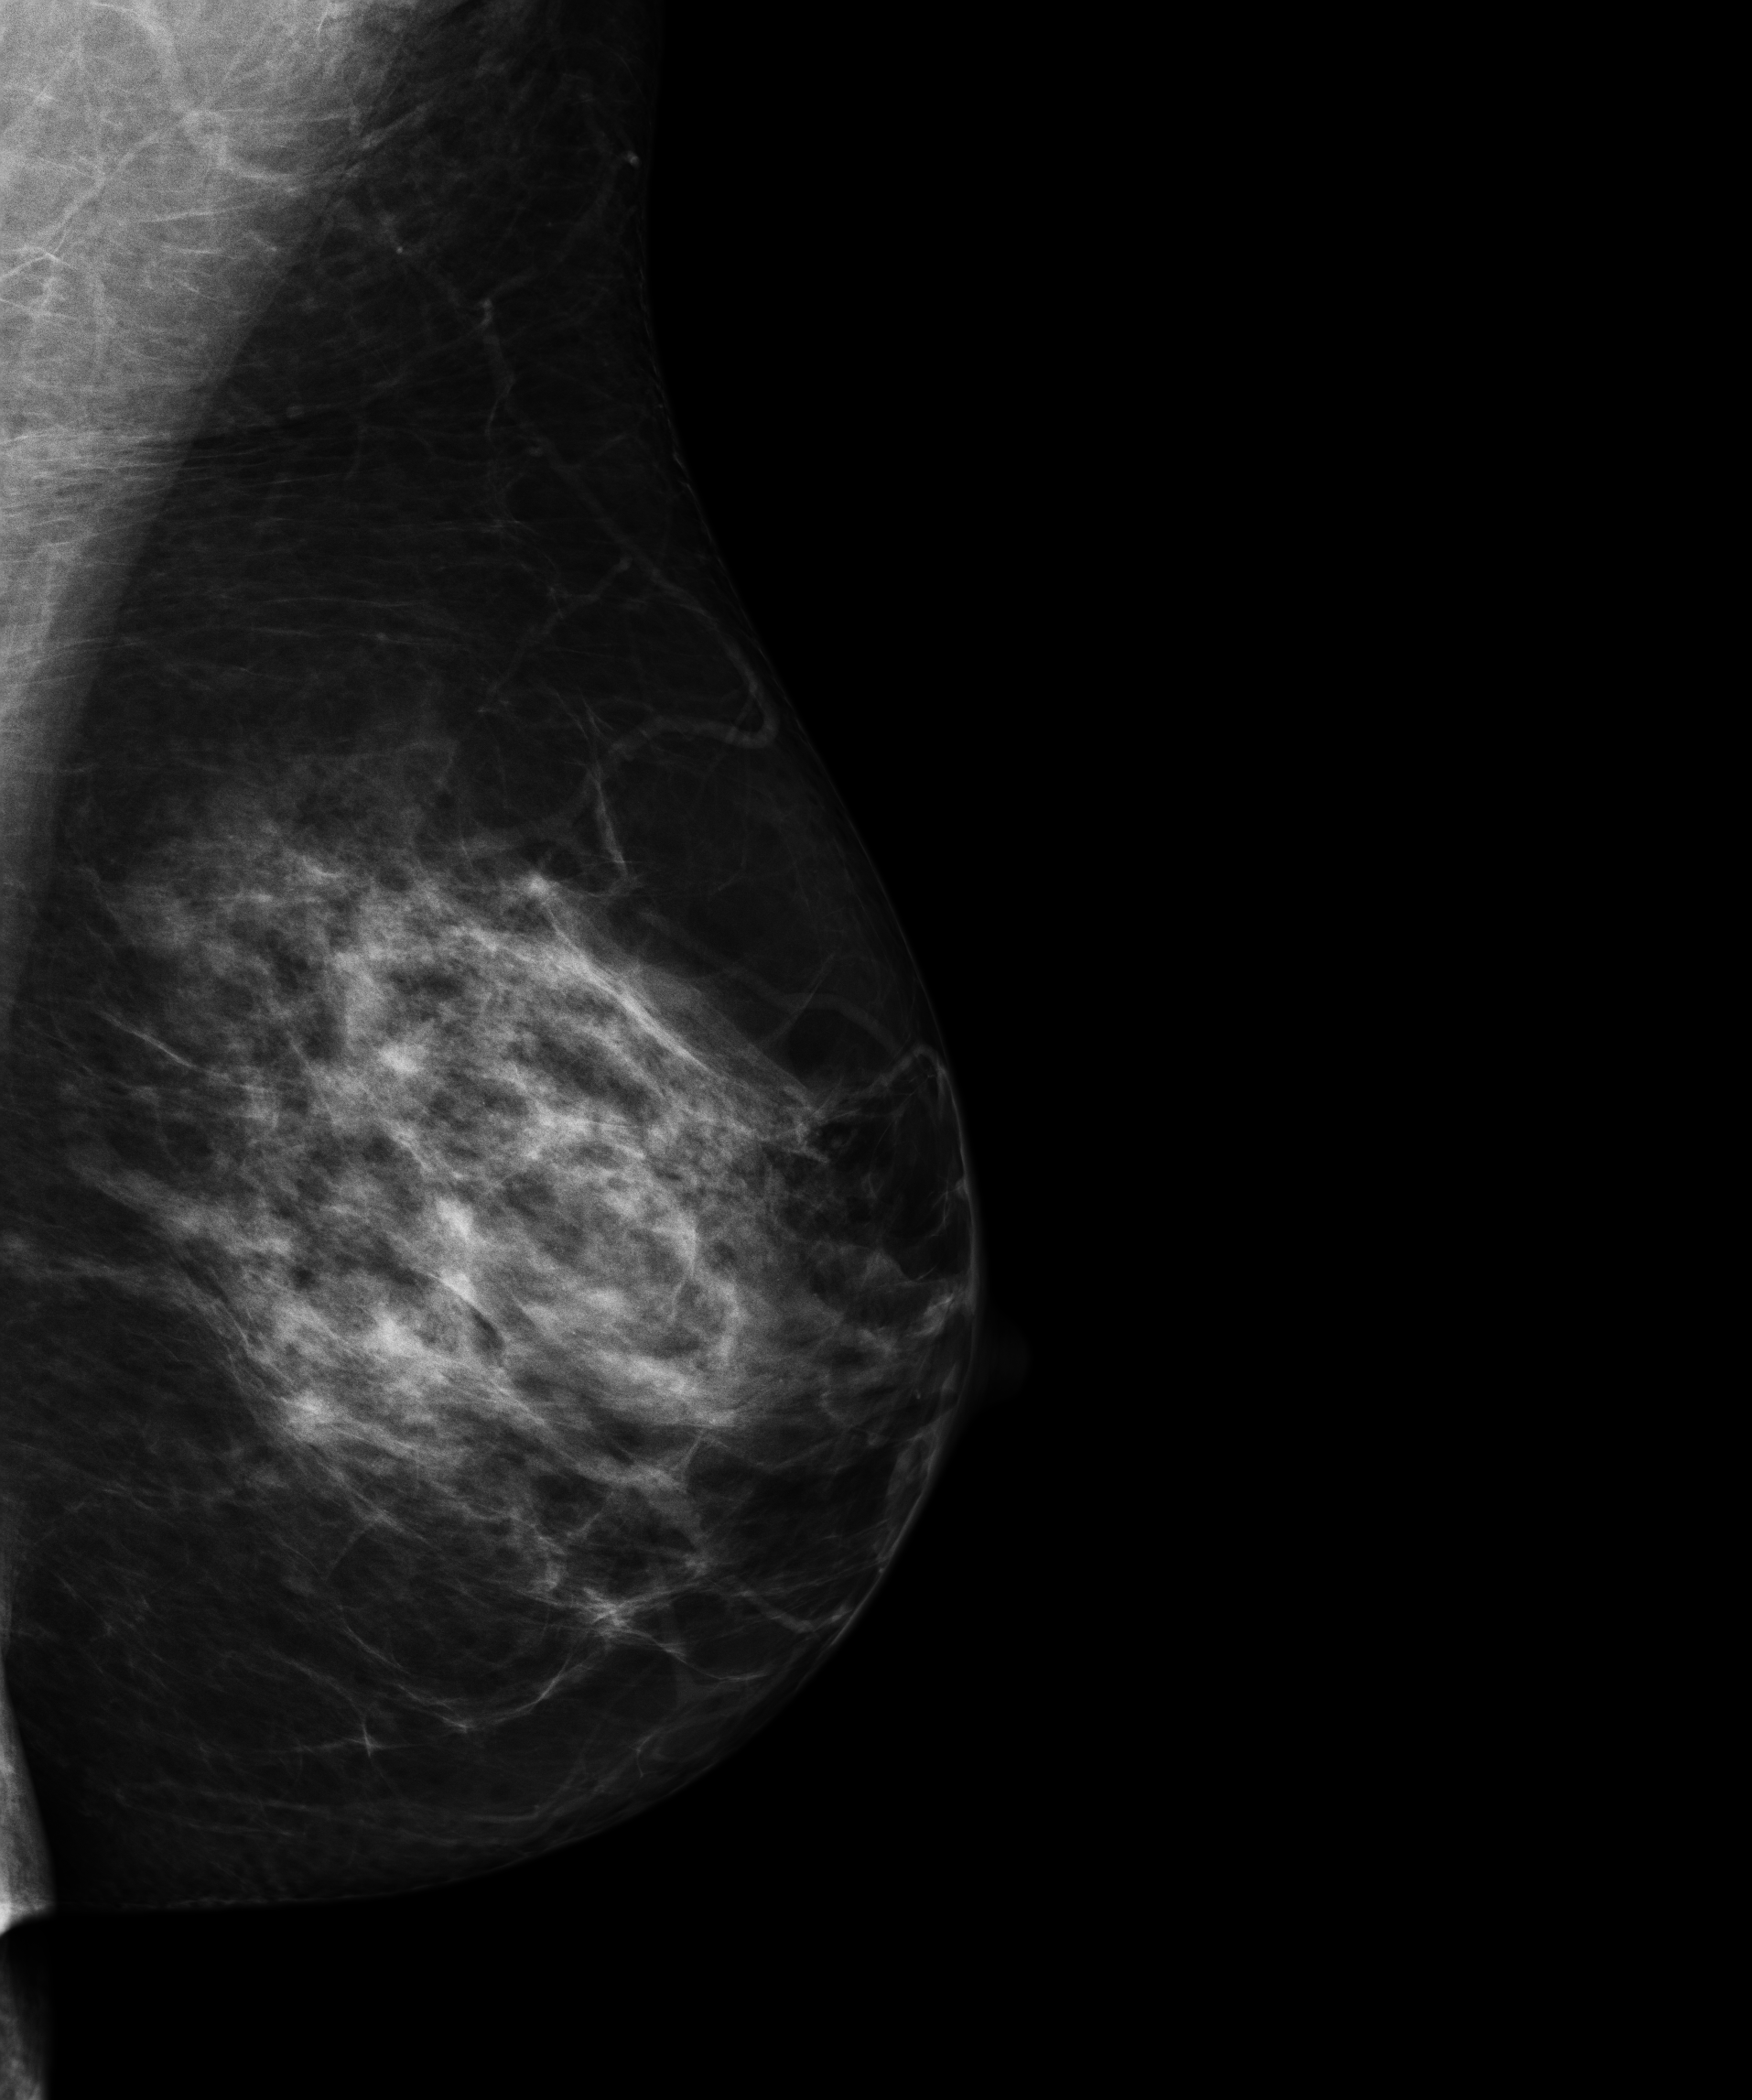
Digital mammogram (FFDM); left breast; MLO view; annual screening mammography examination; compressed breast thickness 70 mm; system: Senographe Essential ADS_56.21.3. Patient aged 45 years (female).
- breast density at the screening exam (both breasts): heterogeneously dense (BI-RADS density category c)
- final BI-RADS category for the screening round (tomosynthesis exam, both breasts): category 1
- recall: no recall after this screen